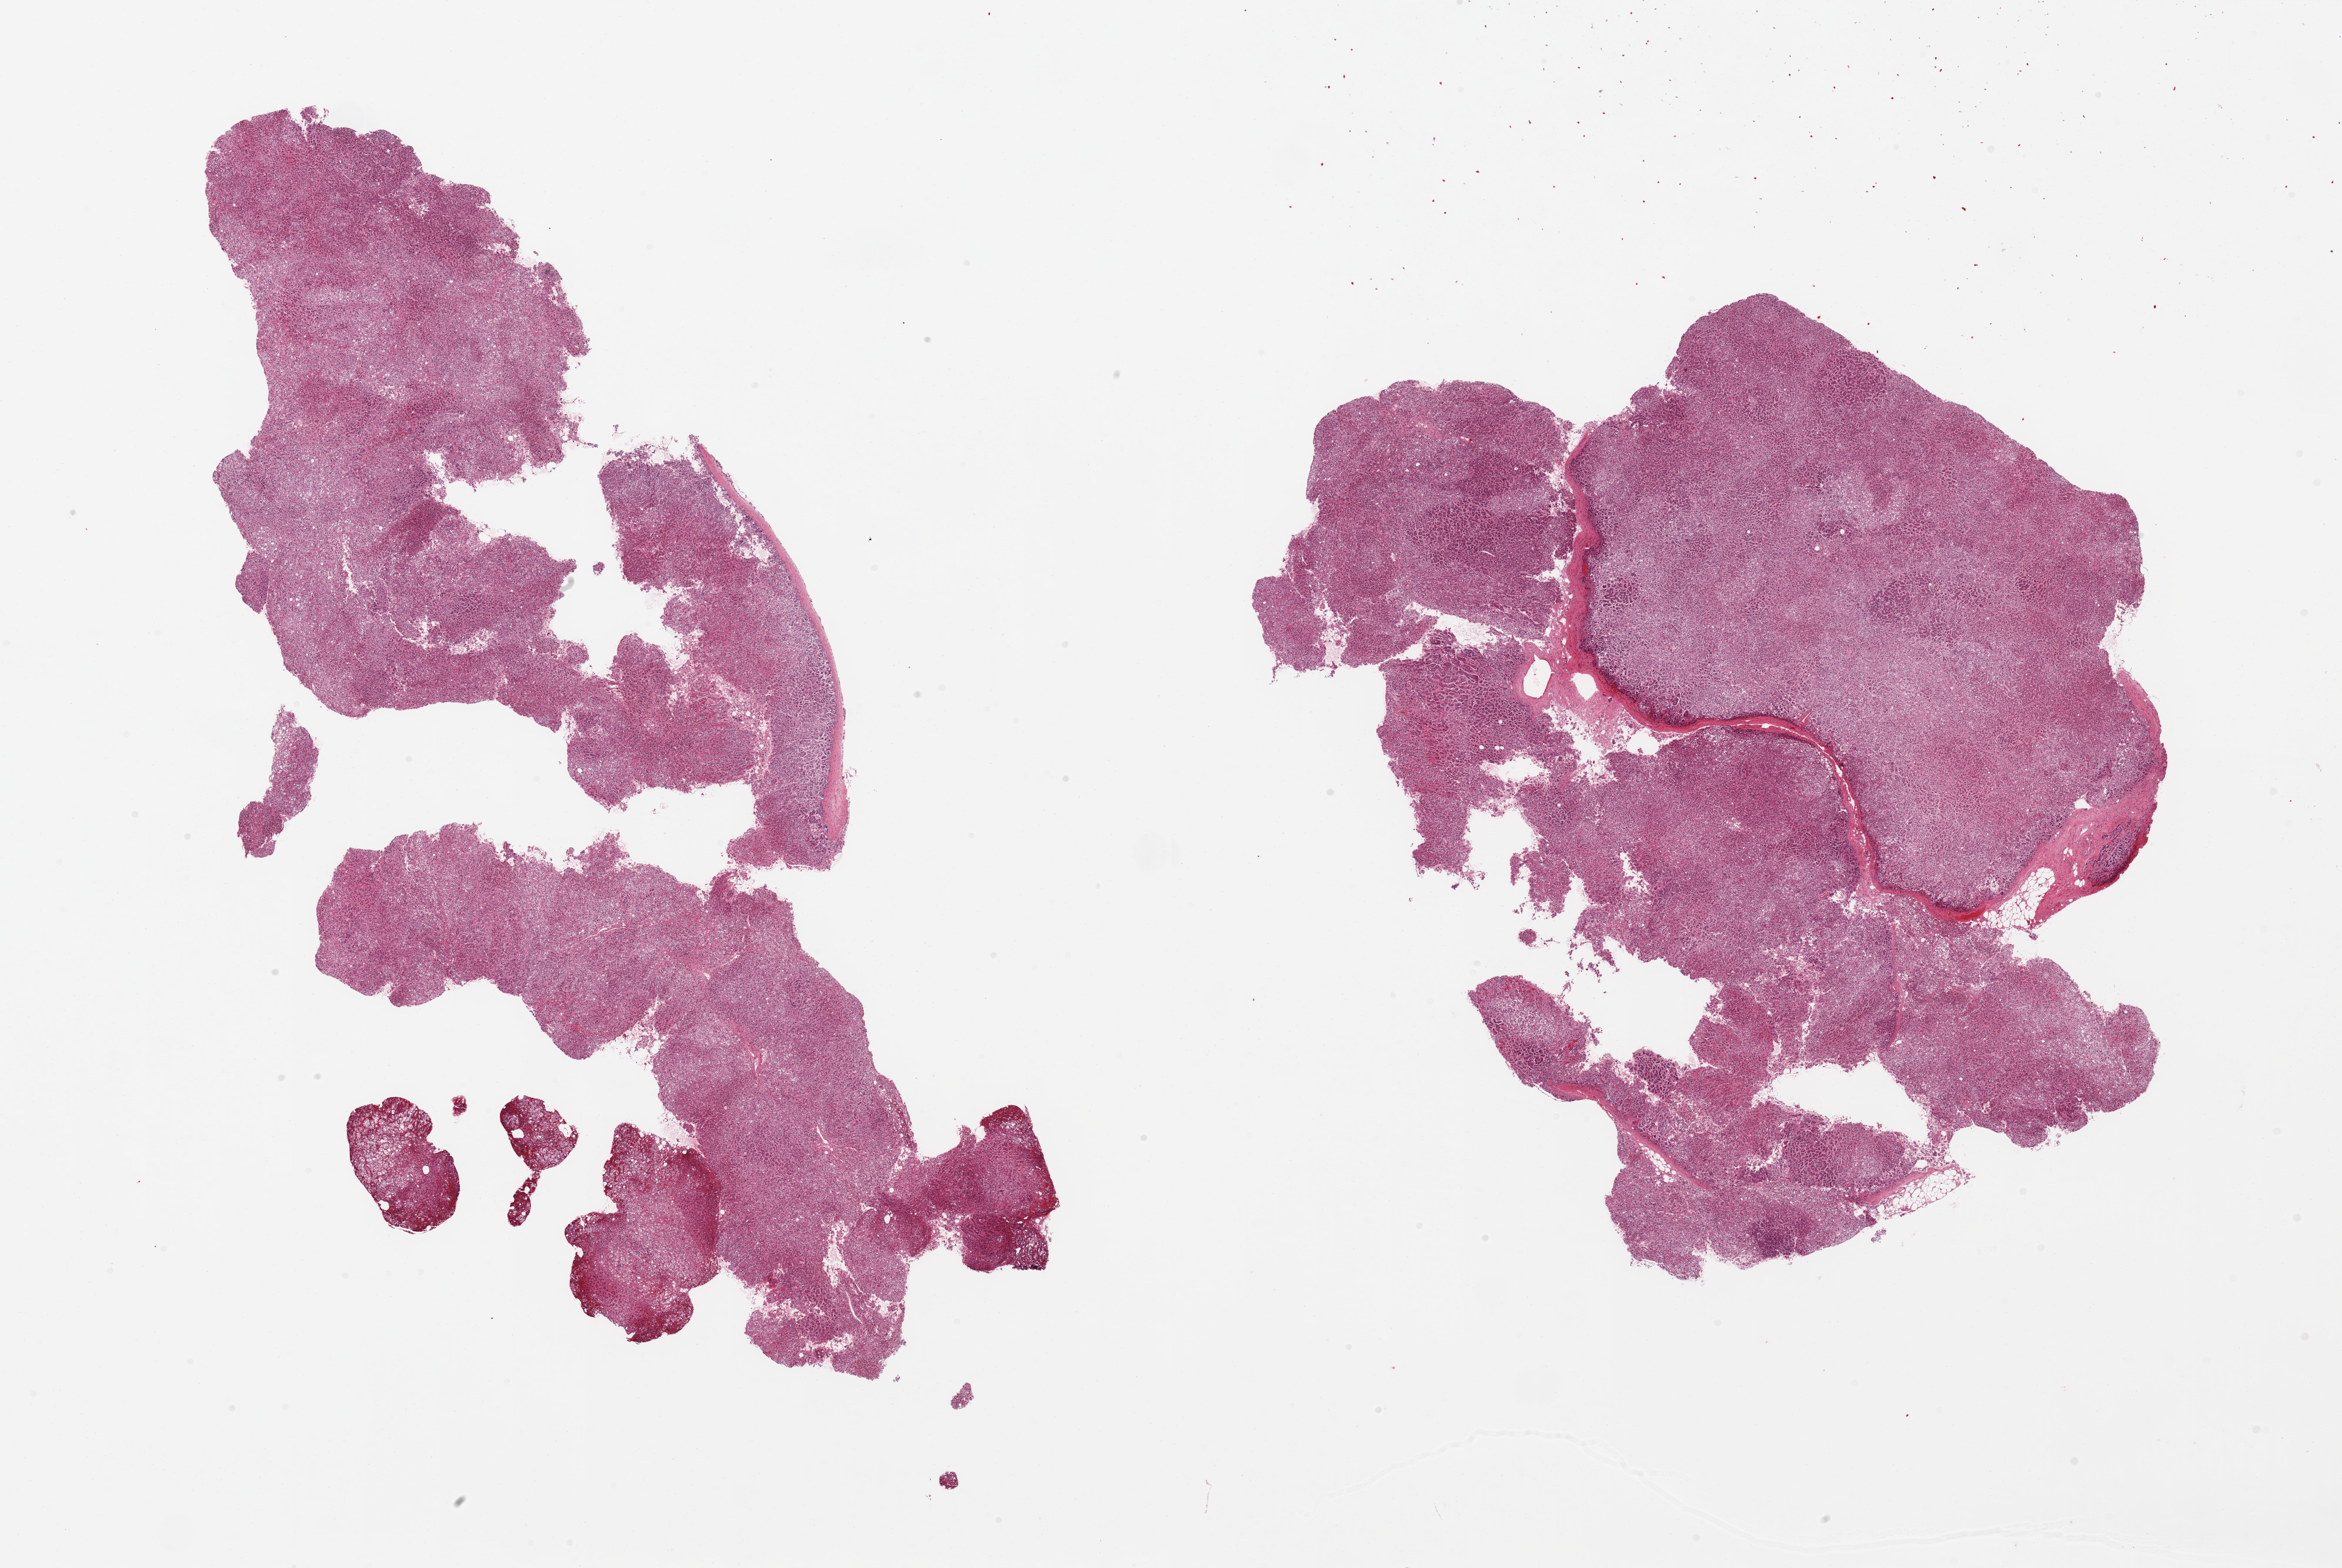
Digitized hematoxylin and eosin (H&E)-stained section, low-resolution overview of the scanned area, about 31.5 x 21.1 mm; PAXgene-fixed, paraffin-embedded tissue; target tissue: adrenal gland; donor tissue sample. Donor sex: male.
Review note (as recorded): 2 pieces, all cortex.